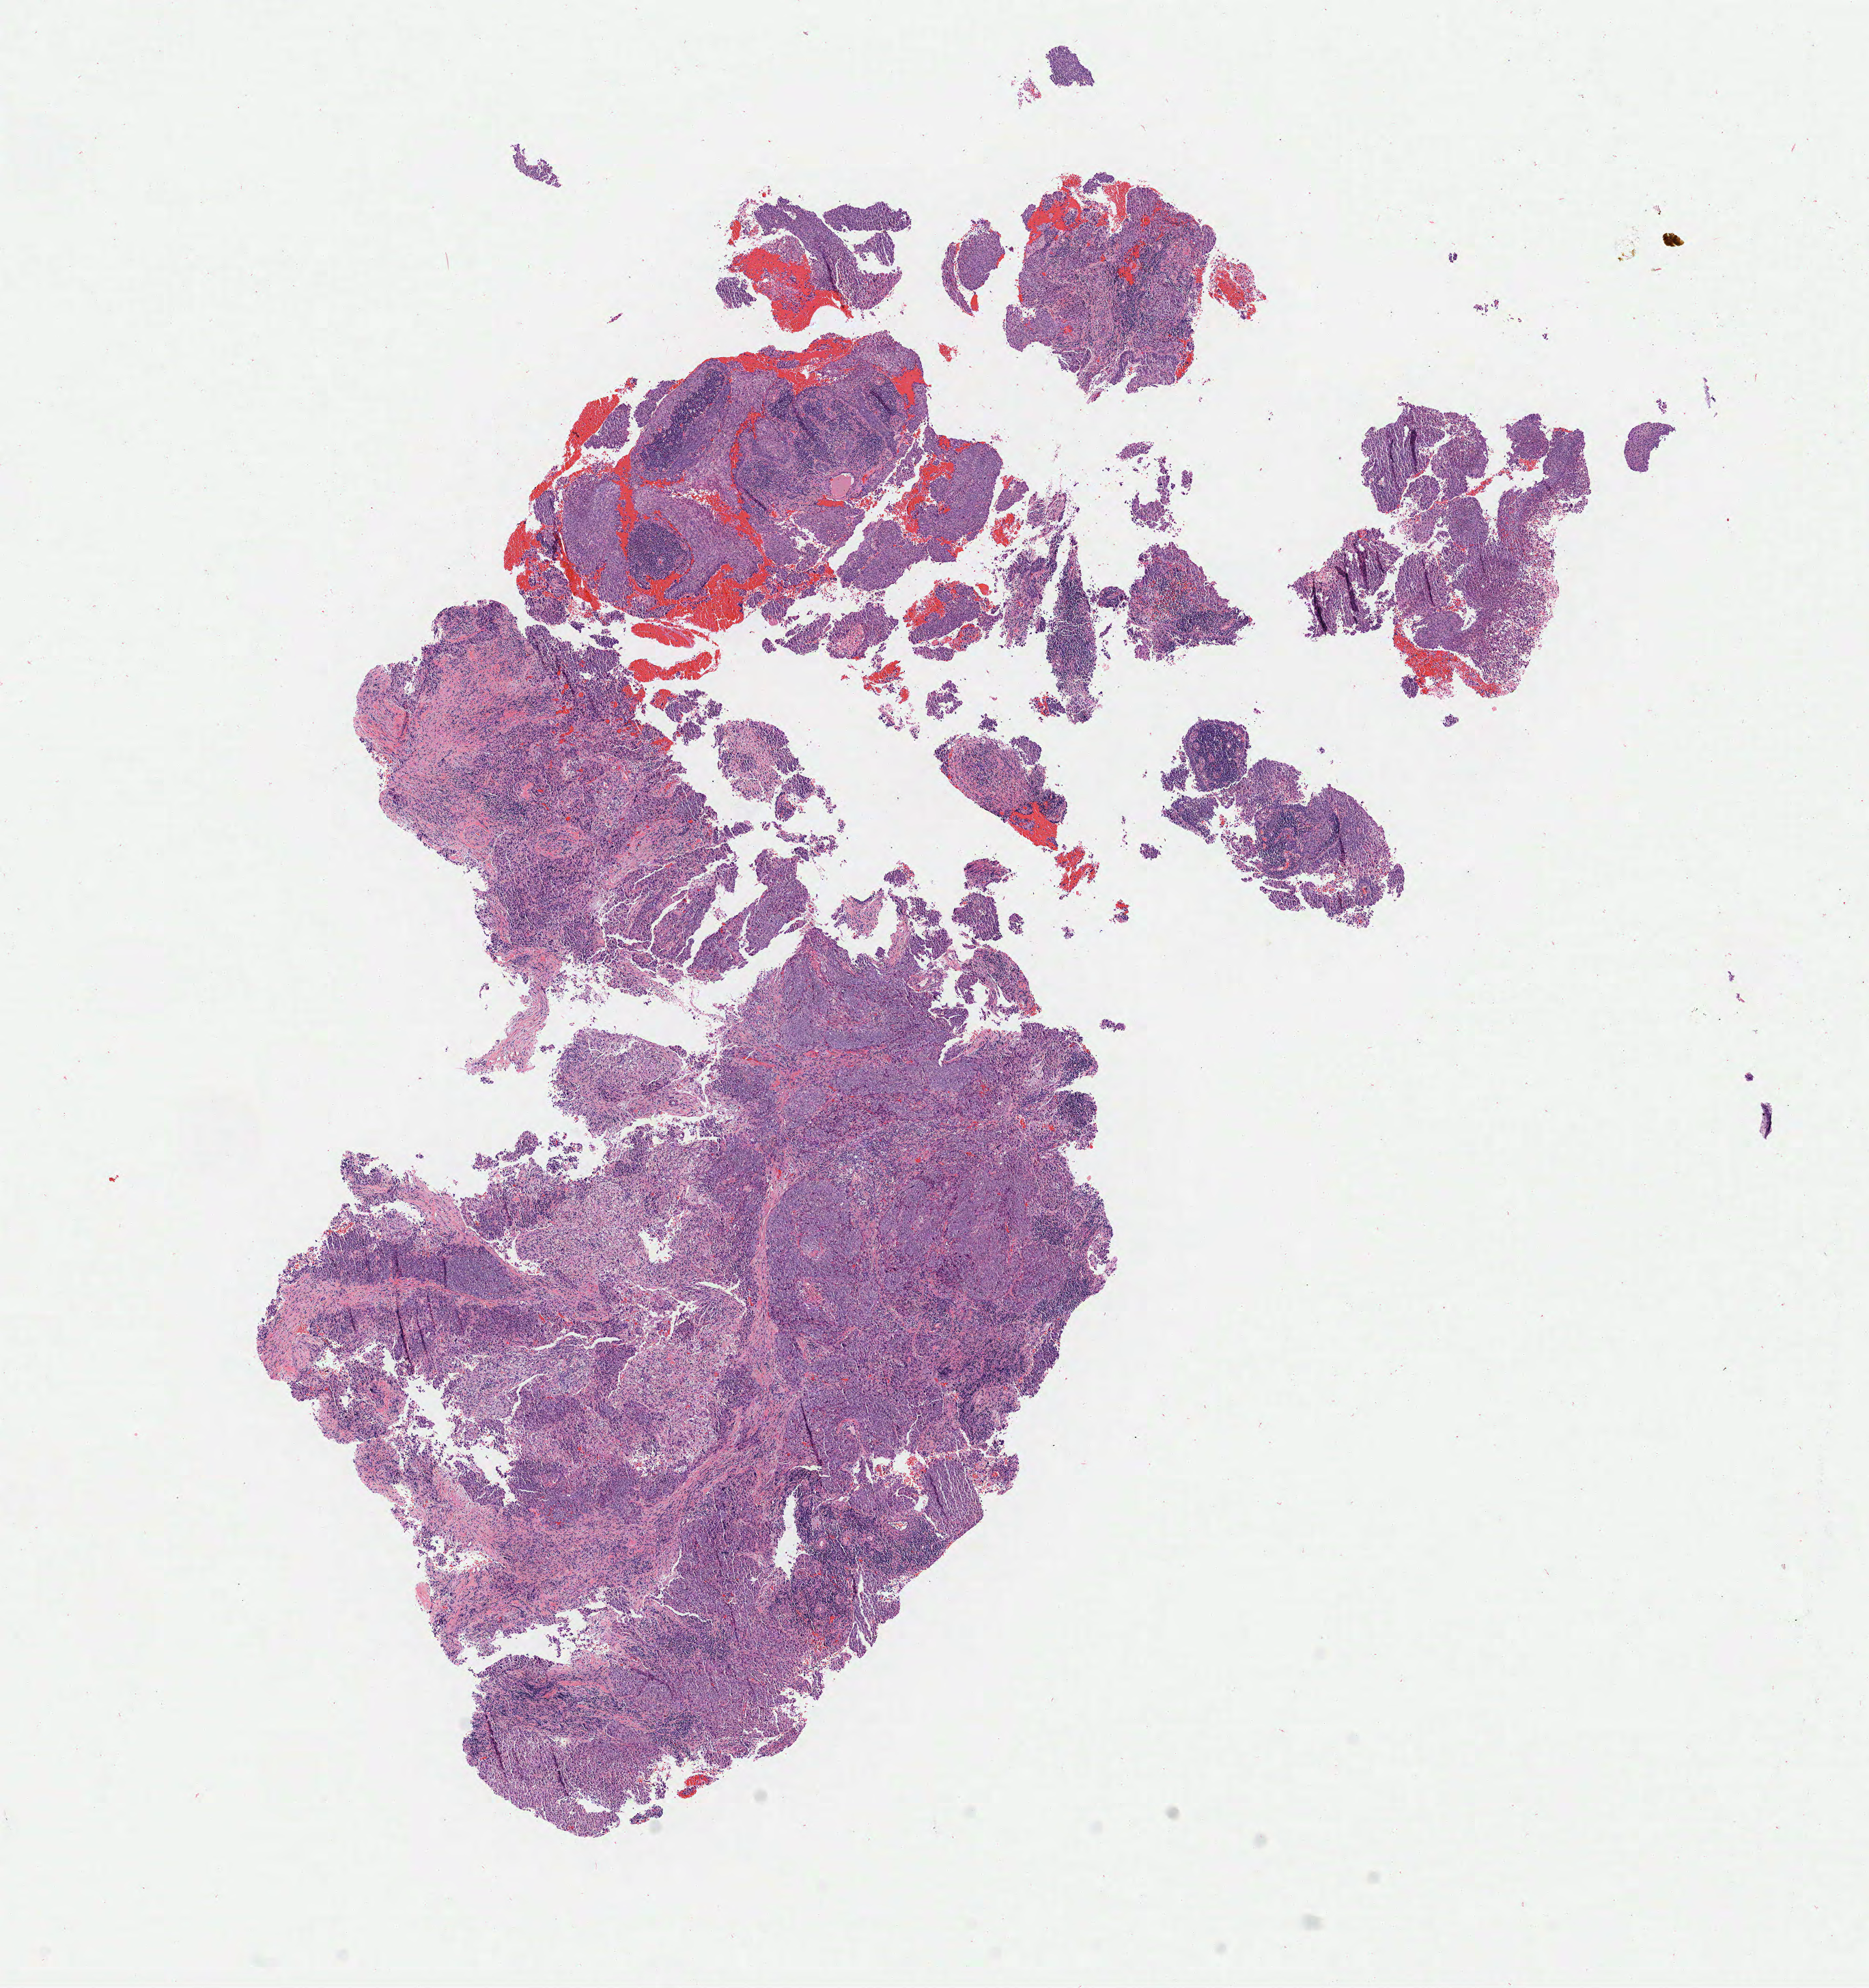
Digitized H&E-stained section — a low-resolution overview of the entire scanned area, about 10.9 x 11.6 mm. Tumor tissue. Site: cervix. Patient: female, 50 years old.
* histologic diagnosis: Squamous cell carcinoma, large cell, nonkeratinizing, NOS